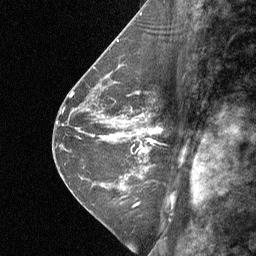
Breast MRI (dynamic contrast-enhanced), one sagittal slice; slice 29 of 64 in the series (ordered by position); dynamic contrast-enhanced study with each time point stored as its own series, time point 2 of 3 at this slice position (early post-contrast, ordered by acquisition time); 1.5 T; TE 4.8 ms, TR 27 ms; 256 × 256 image matrix, field of view 180 × 180 mm. Patient: female, 42 years. From the clinical record (not read from this slice): setting: breast cancer imaged before/during neoadjuvant chemotherapy; receptor status: triple-negative.
Structures marked on this image (semi-automatically segmented with operator editing):
- analysis volume of interest (the breast-tissue region the enhancement analysis was run in; not a lesion): box from (x=124, y=106) to (x=175, y=161) px
- tumour enhancement mask (voxels above the 90 % enhancement threshold inside the analysis volume of interest): (x=149, y=129)–(x=157, y=133)